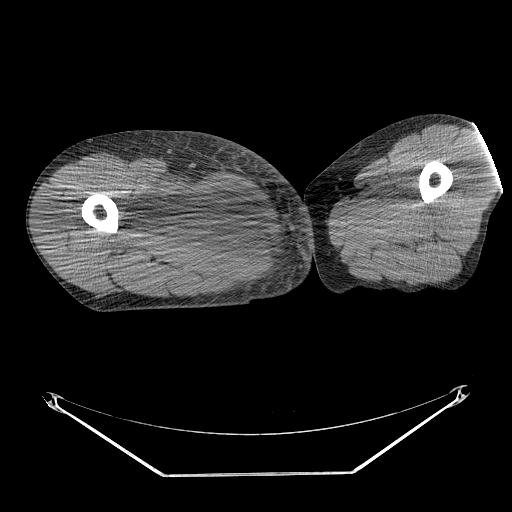
CT of an extremity soft-tissue mass (from a PET/CT study), one axial slice; slice 245 of 311 in the series (ordered by position); soft-tissue window (W 400 / L 40 HU); 3.75 mm slice thickness; 512 × 512 image matrix, field of view 500 × 500 mm. Male patient. Case-level facts recorded for this patient, not image findings: histological type: undifferentiated - pleiomorphic; grade: high; site of the primary tumour: right thigh.
Outlined on this slice (expert contour drawn on MRI and transferred to this co-registered scan by the dataset authors):
- gross tumour volume including surrounding oedema: bounding box [x1, y1, x2, y2] px = [130, 176, 236, 254]
- gross tumour volume (mass): [160, 183, 236, 252]